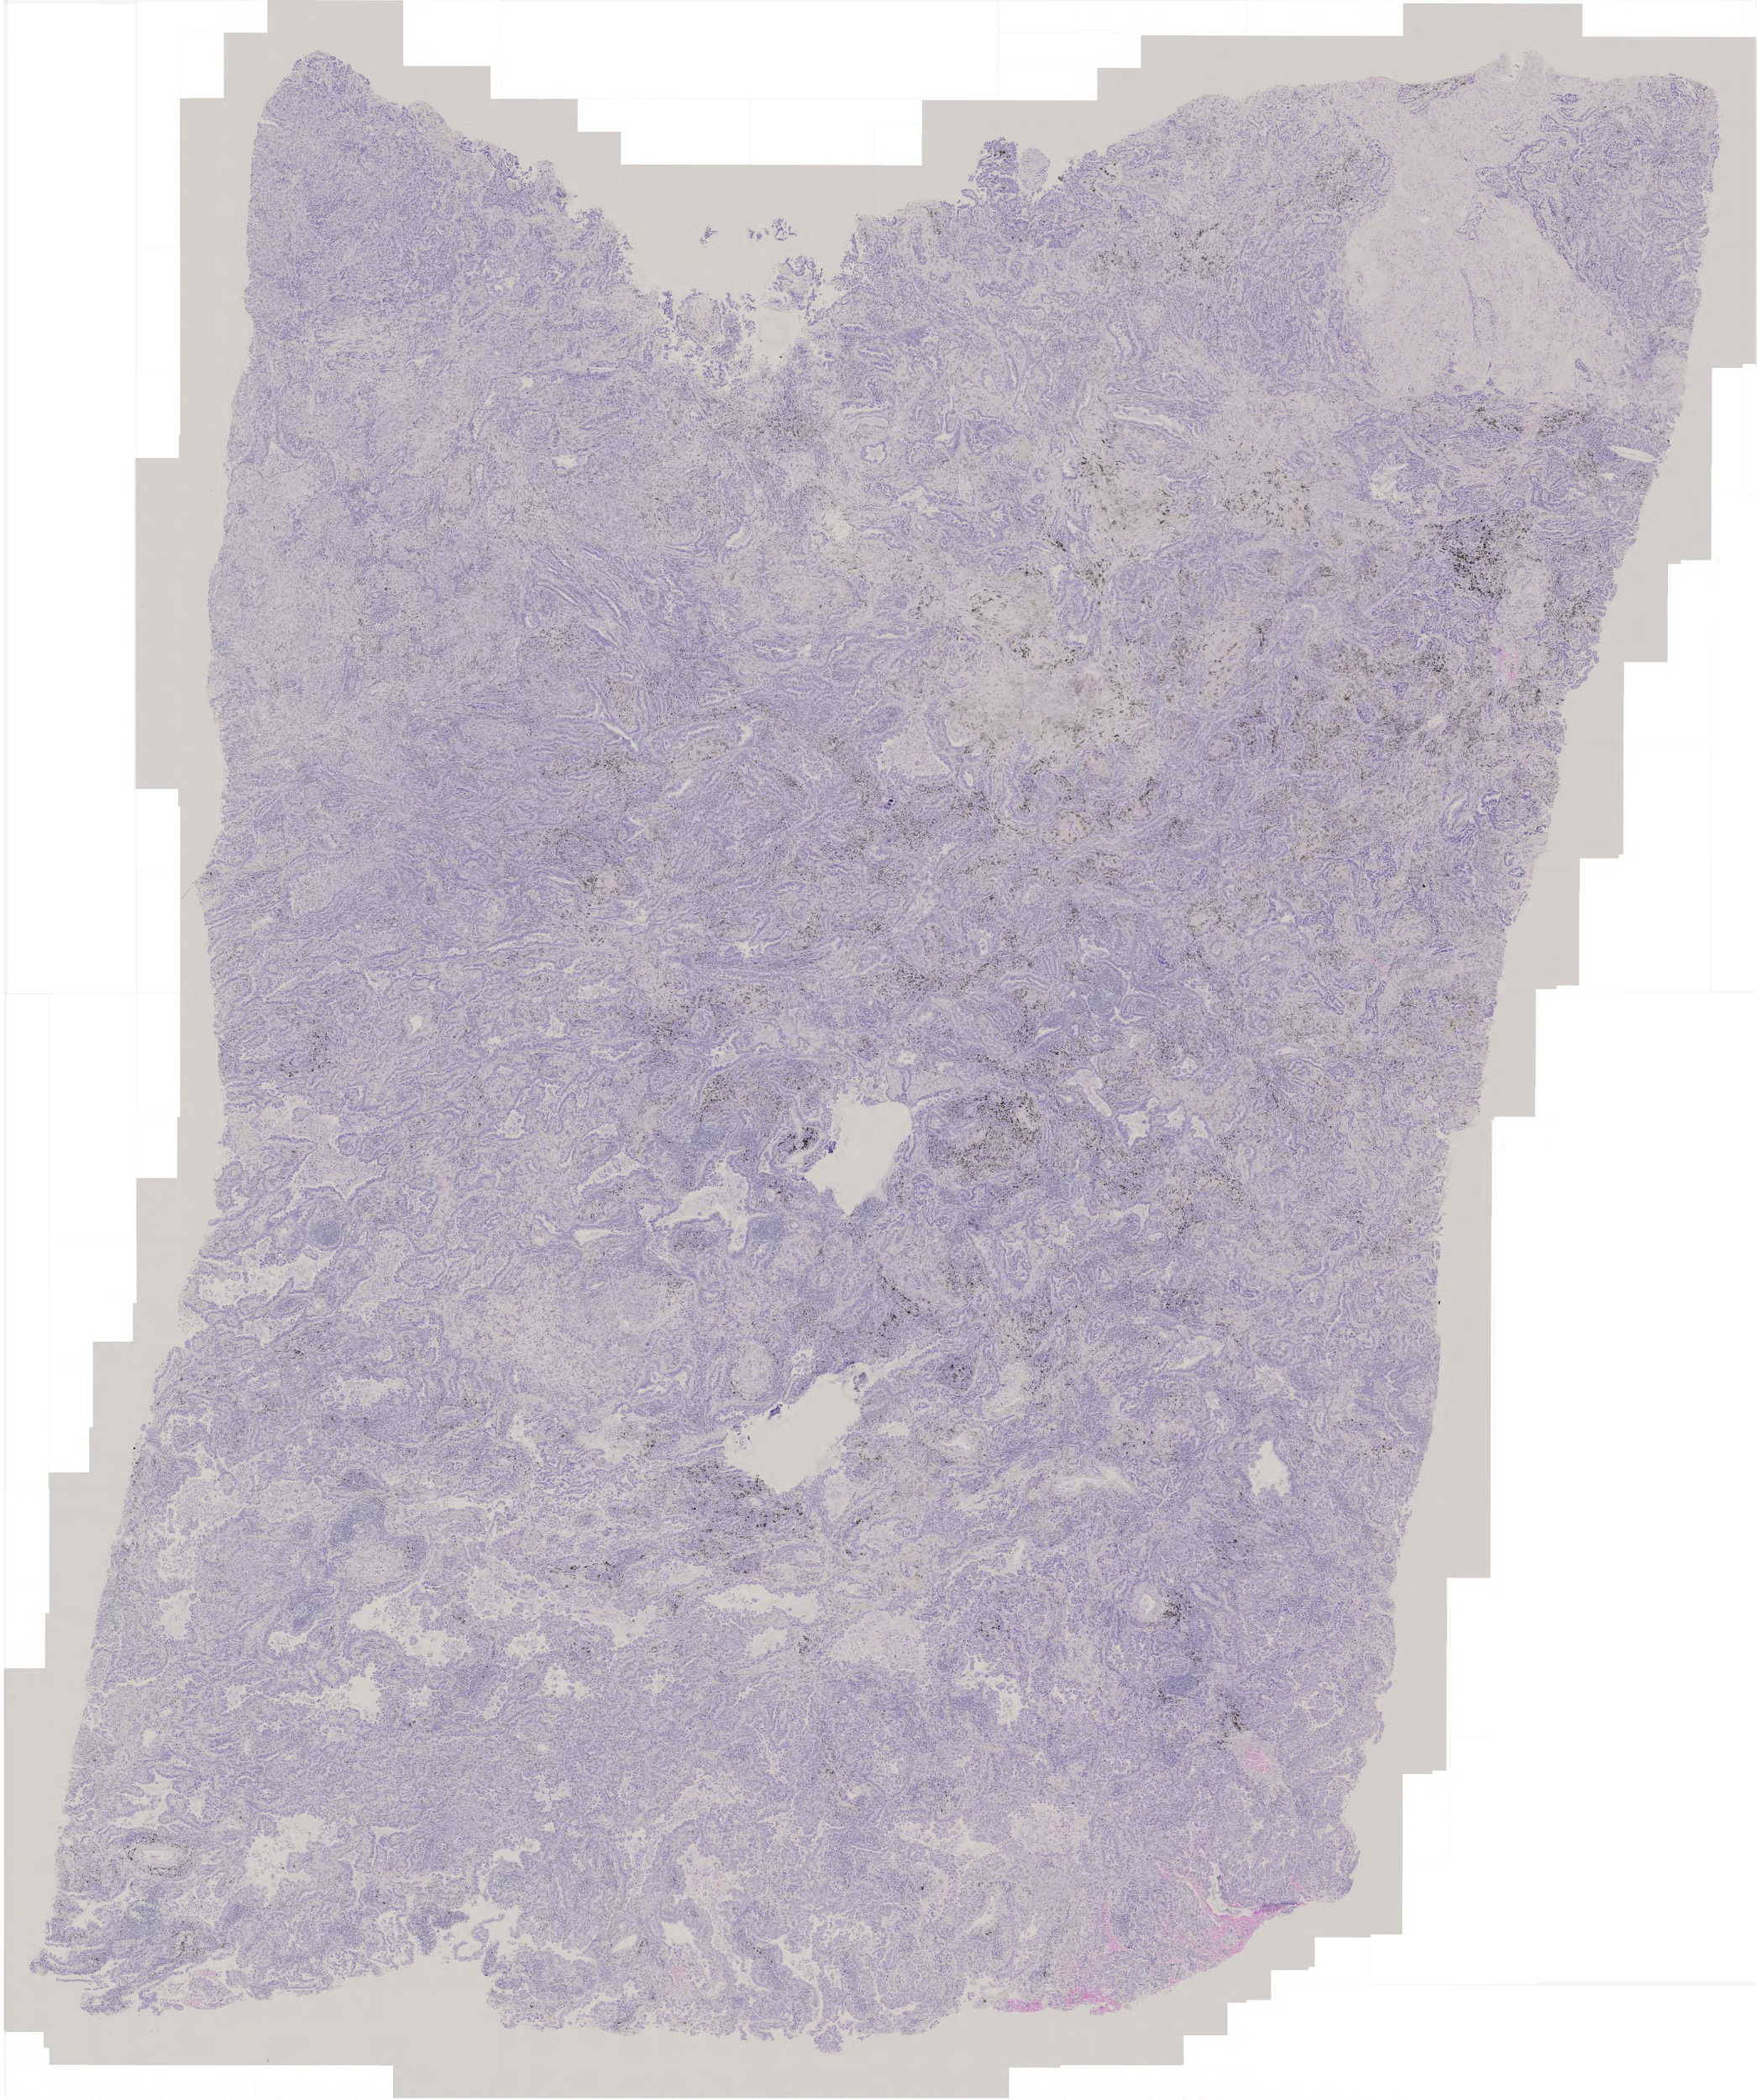
Digitized Hematoxylin and eosin (H&E) stained tissue section (whole slide), shown as a low-resolution overview of the whole scanned area (about 4.2 x 5.0 mm). Formalin-fixed paraffin-embedded (FFPE) diagnostic section. Primary tumour sample from the lung. Patient: male, age at initial diagnosis 62 years.
Pathologic diagnosis: Adenocarcinoma with mixed subtypes. Laterality: left. AJCC pathologic stage: IB (6th edition).